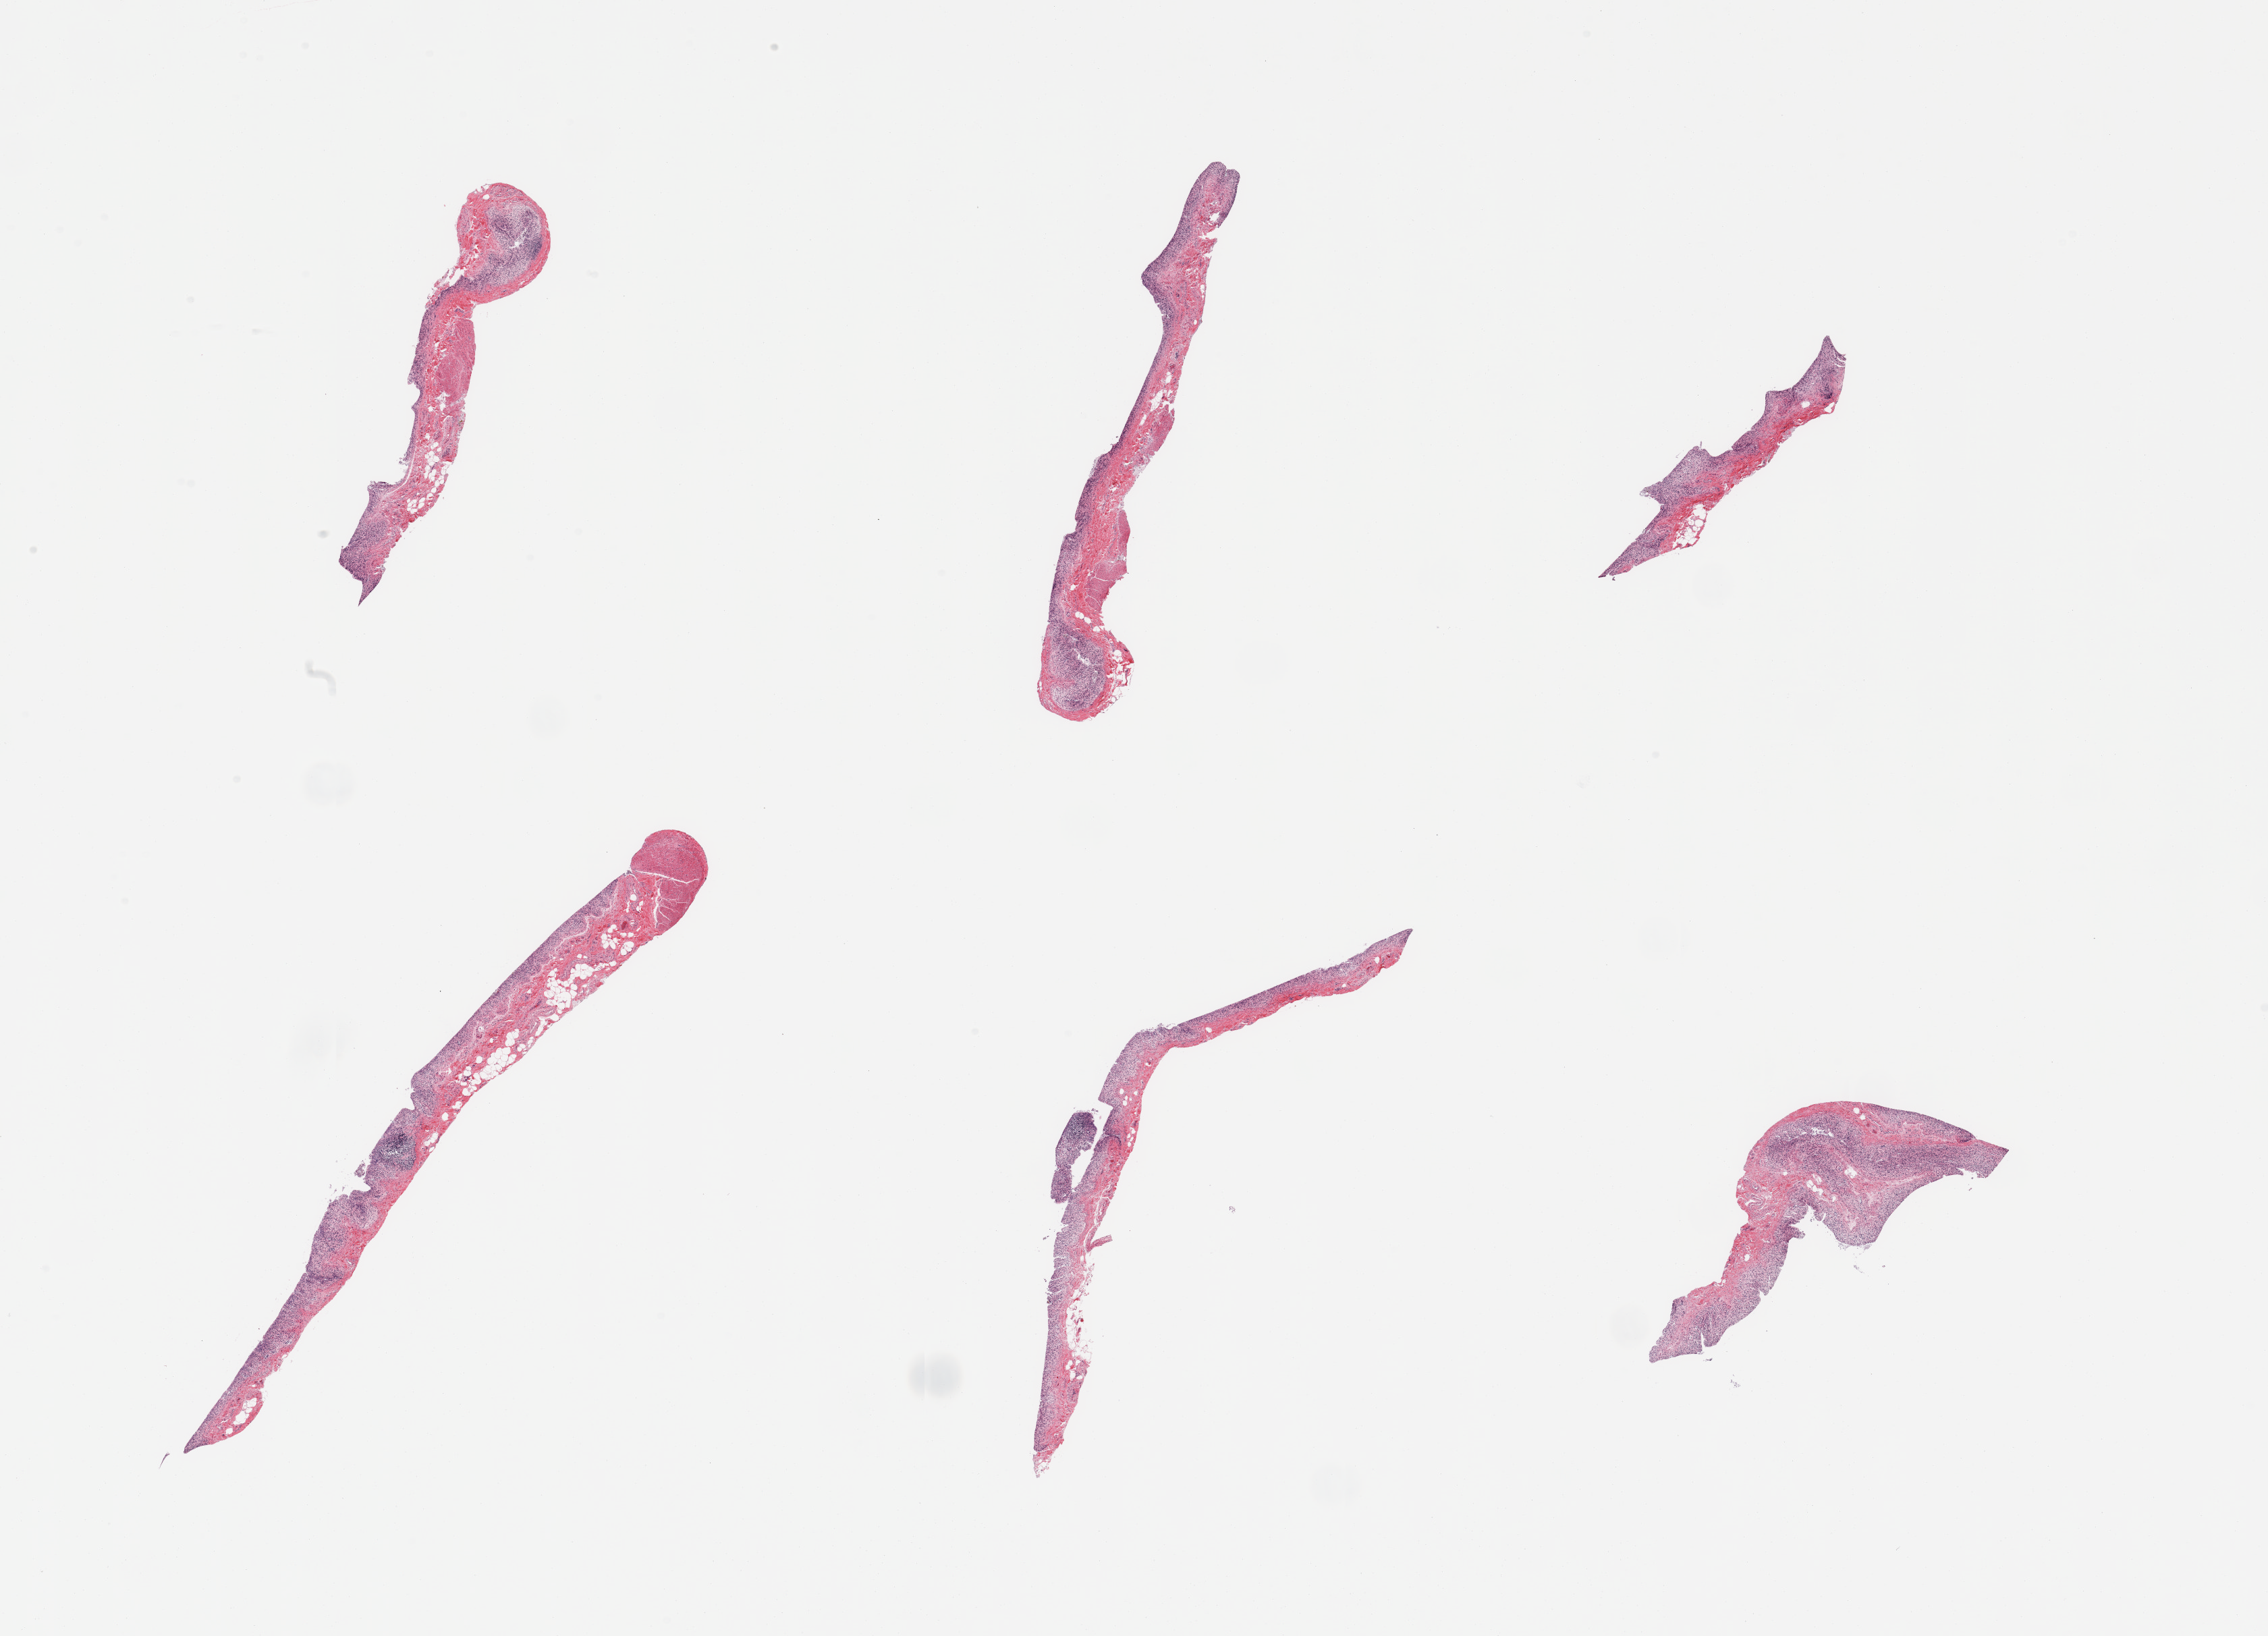
Digitized H&E-stained section, low-resolution overview of the scanned area, about 26.6 x 19.2 mm (from a 20x scan); PAXgene-fixed, paraffin-embedded tissue; target tissue: transverse colon; donor tissue sample. Donor: male.
• review note (as recorded): 6 pieces; severely autolyzed mucosa and preserved focal thin layer of muscularis on 3 of 6 sections